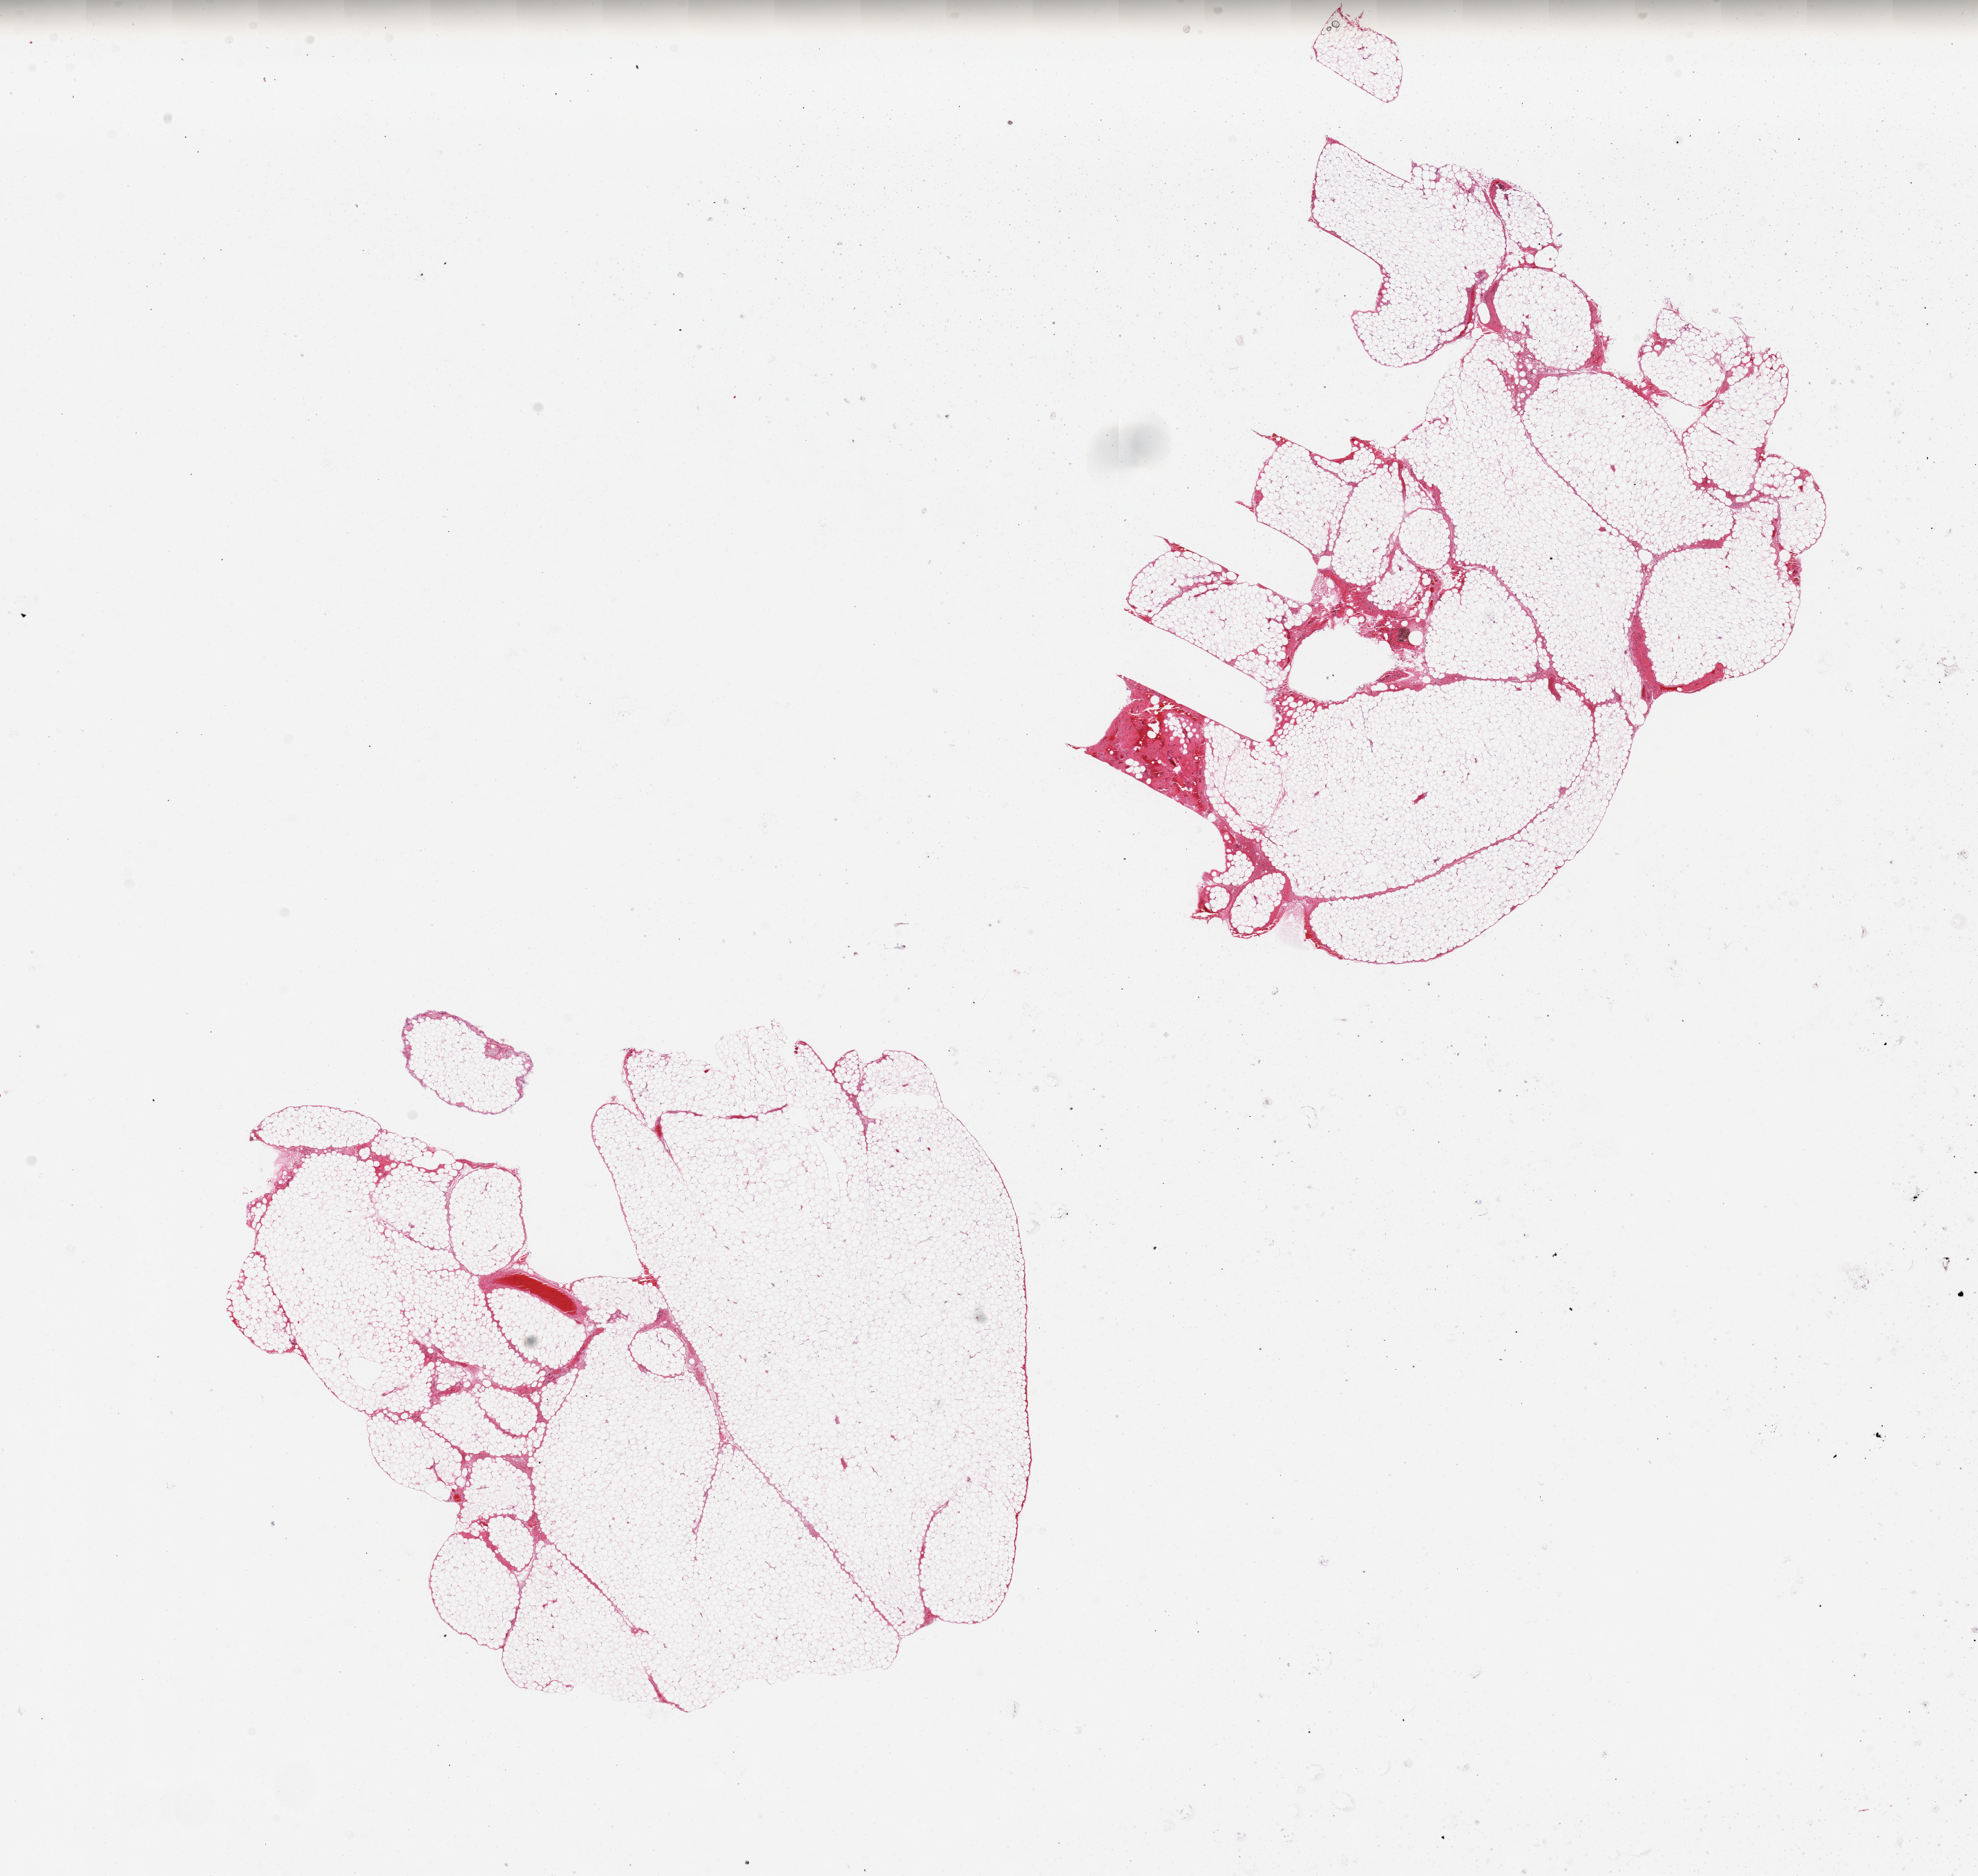
Whole-slide image, haematoxylin and eosin stain — low-resolution overview of the scanned area, about 22.6 x 21.5 mm. PAXgene-fixed paraffin-embedded (PFPE) section. Section of omentum (target tissue). Tissue donor sample. Female donor.
- pathologist's review note for this sample: 2 pieces